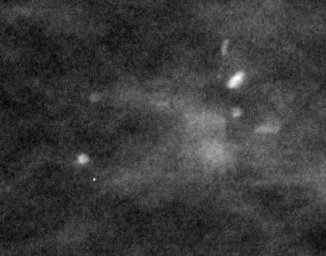
Region of interest cut from a scanned film mammogram (one marked finding); left breast; MLO view.
Marked abnormality: calcifications, morphology pleomorphic, distribution clustered; BI-RADS assessment category 4; subtlety rating 4 on a 1 (subtle) to 5 (obvious) scale; pathology result (as recorded, not read from the image): malignant.